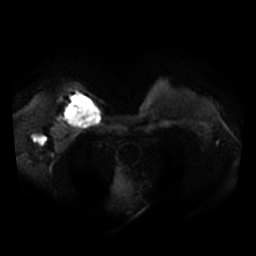
Breast MRI, one axial slice. Slice 28 of 36 in the series (ordered by position). Diffusion-weighted series; image 2 of 4 stored at this slice position (different b-values; order by instance number). 3 T. 5 mm slice thickness. 256 × 256 image matrix. Female patient.
Annotated regions visible in this slice (expert manual segmentation):
- tumour on diffusion-weighted imaging: bounding box (x1, y1, x2, y2) in pixels: (65, 96, 99, 126)